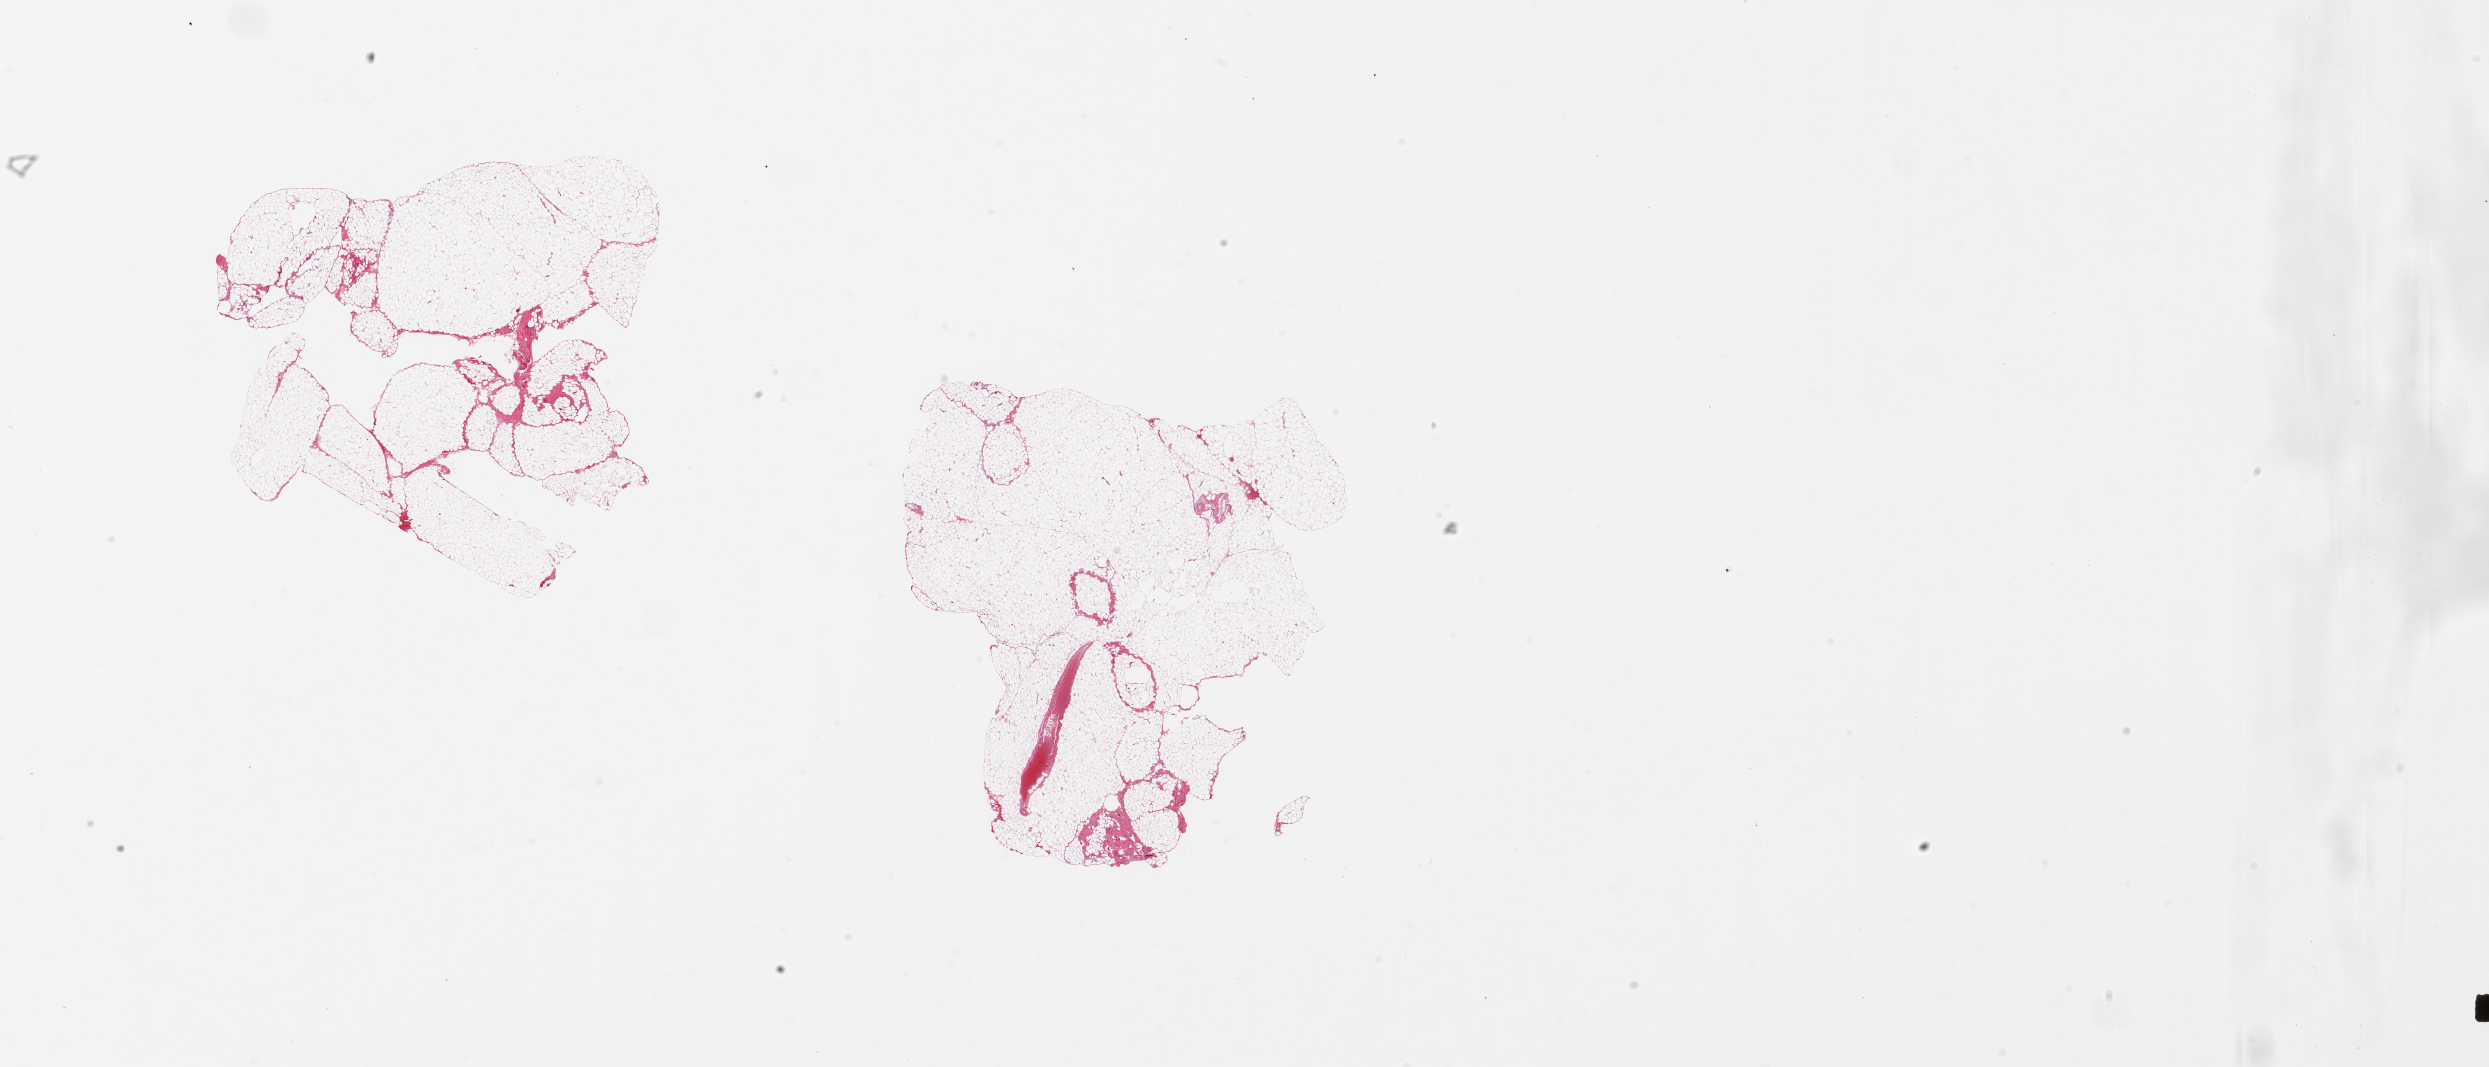
Hematoxylin and eosin (H&E) whole-slide image — low-resolution overview of the scanned area, about 39.4 x 16.9 mm (slide scanned at 20x). PAXgene-fixed, paraffin-embedded tissue. Section of omentum (target tissue). Donor tissue sample. Donor sex: female.
Review note (as recorded): 2 pieces. 8x8 7 8x7mm; well fixed.